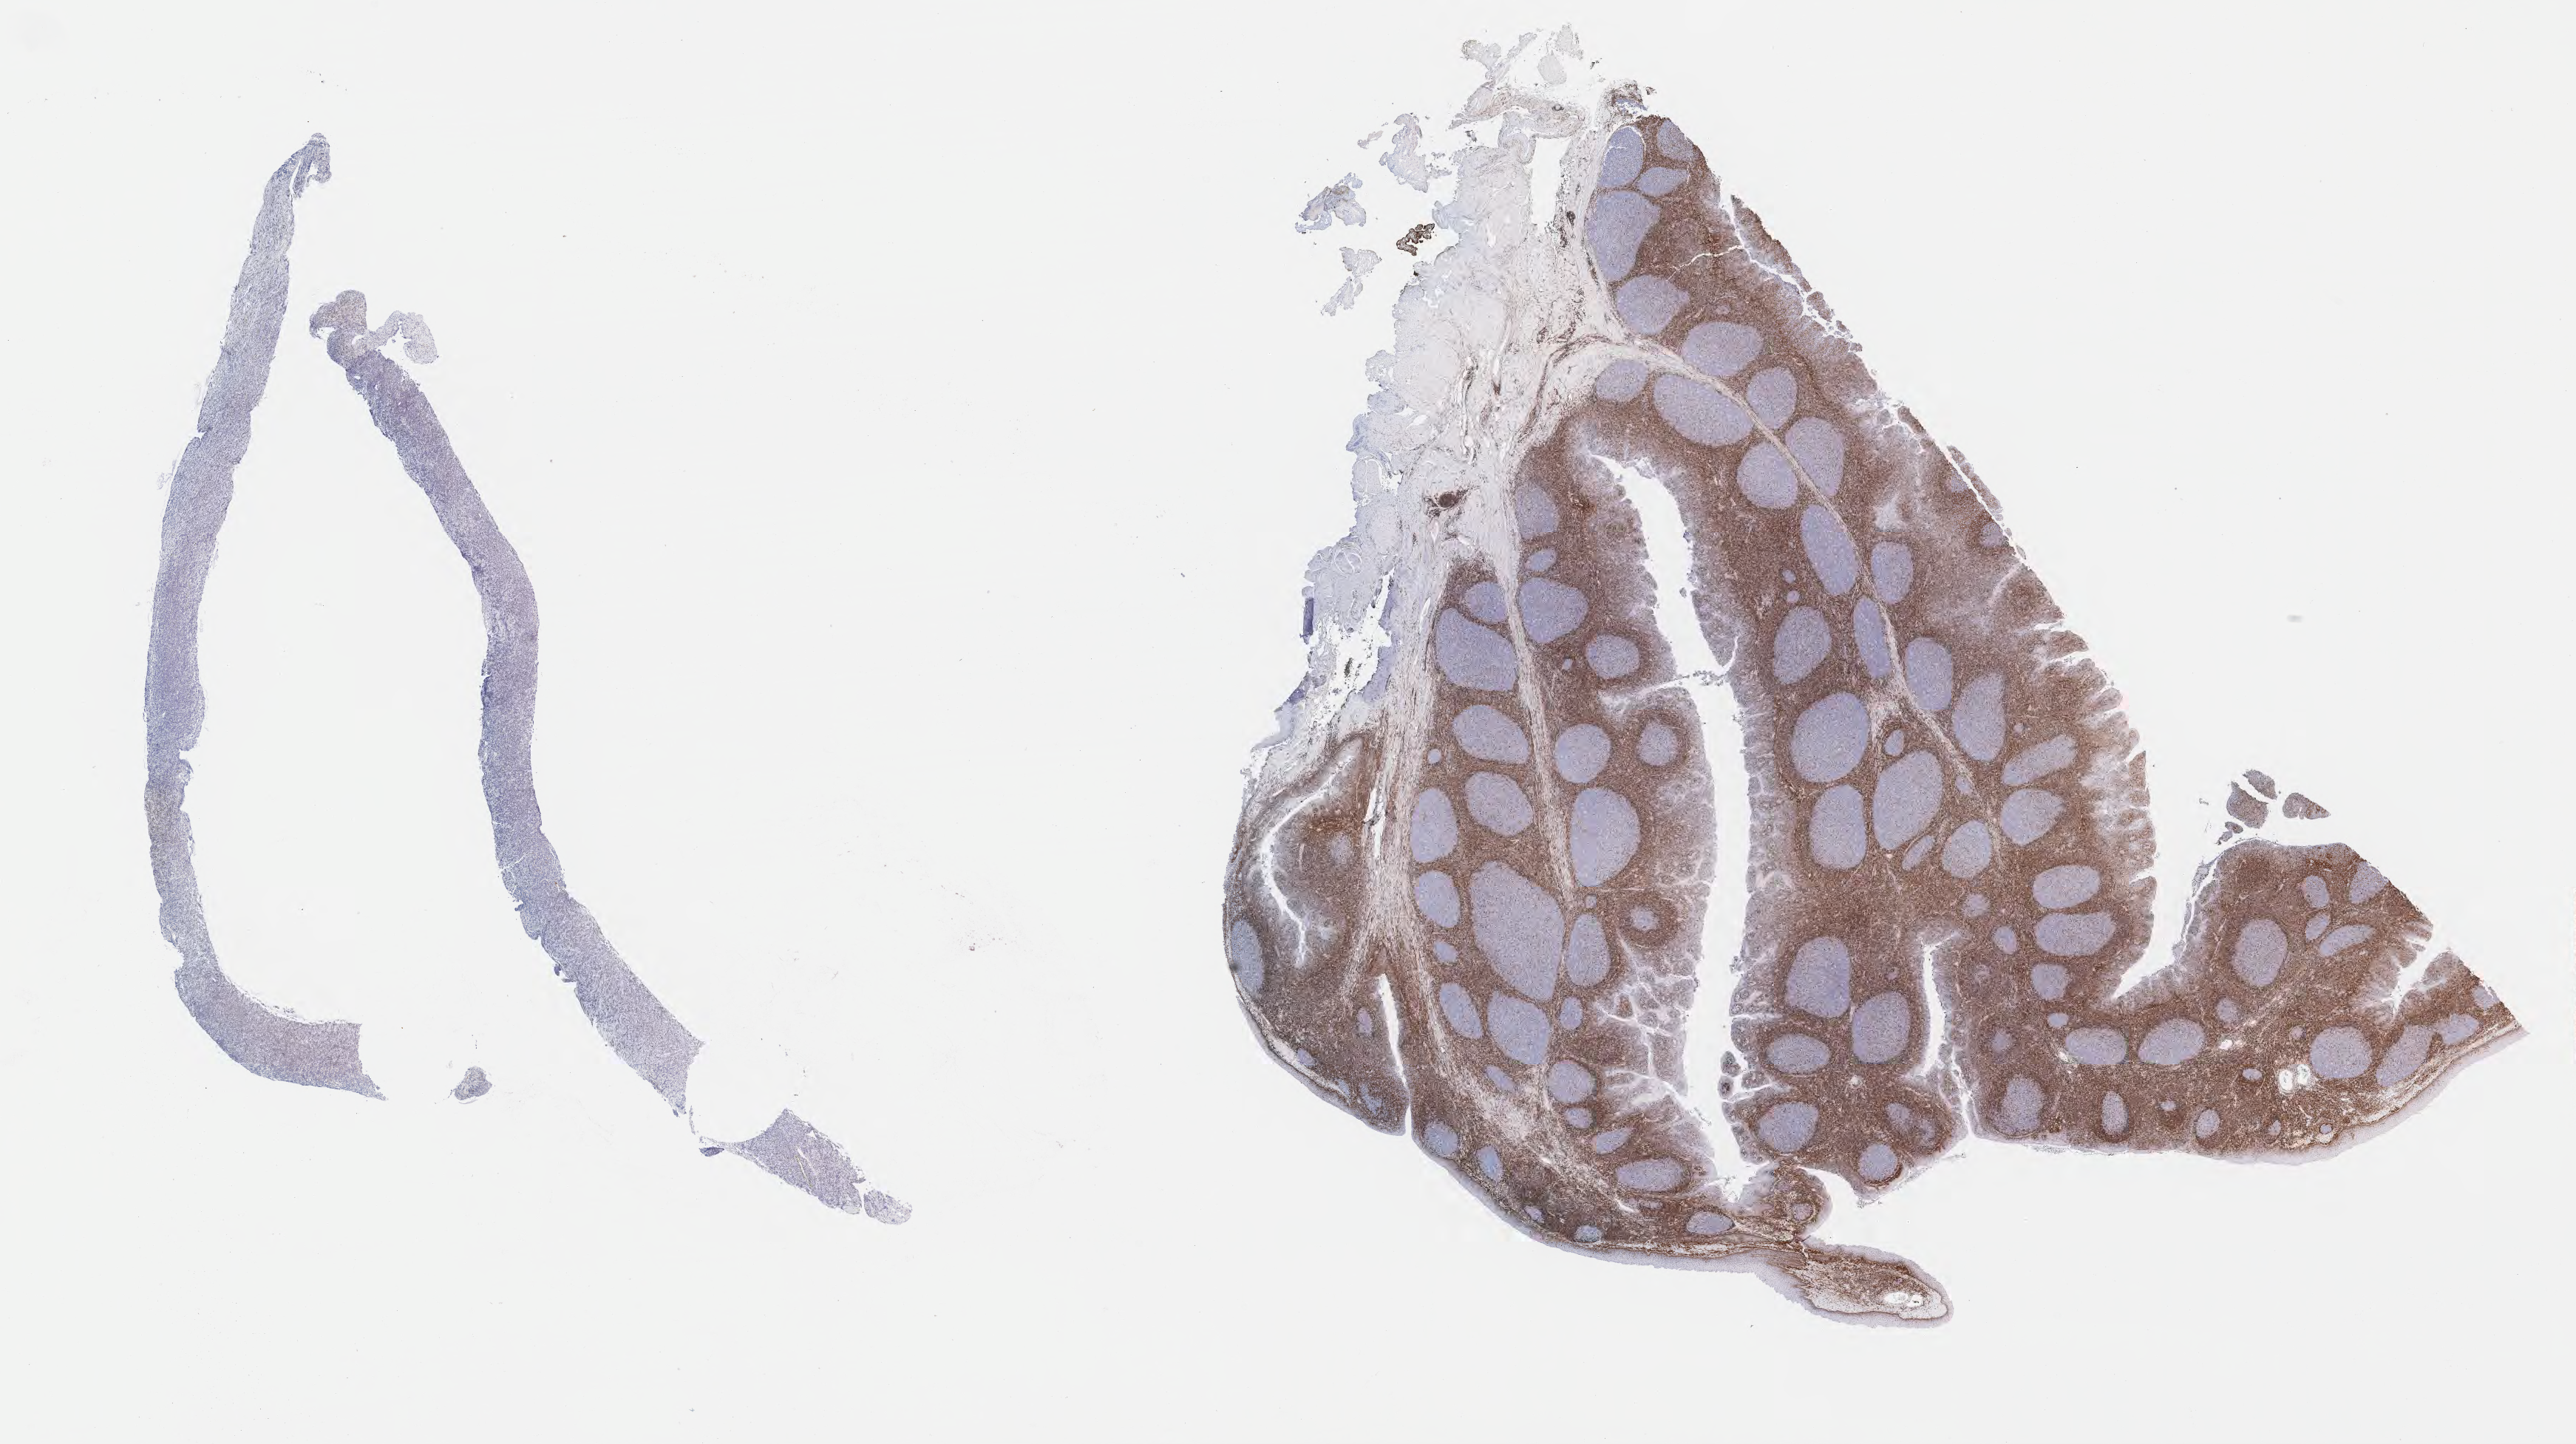
Whole-slide image, immunohistochemical stain for BCL2, a low-resolution overview of the entire scanned area, about 28.2 x 15.8 mm; tumor tissue; anatomic site: abdomen proper. Male patient; age at initial diagnosis 9 years.
- diagnosis: Burkitt lymphoma, NOS